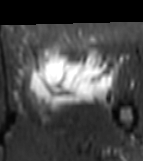
MRI of an extremity soft-tissue mass, one axial slice; position 34 of 81 along the scan axis; STIR; MR volume resampled by the dataset authors to the PET/CT grid (not the native acquisition matrix); 143 × 161 image matrix, field of view 140 × 157 mm. Female patient. From the clinical record (not read from this slice): histological type: myxofibrosarcoma; grade: intermediate; site of the primary tumour: left thigh.
Structures marked on this image (expert contour drawn on MRI and transferred to this co-registered scan by the dataset authors):
- gross tumour volume including surrounding oedema: bounding box [x1, y1, x2, y2] px = [26, 44, 118, 118]
- gross tumour volume (mass): [28, 44, 114, 102]